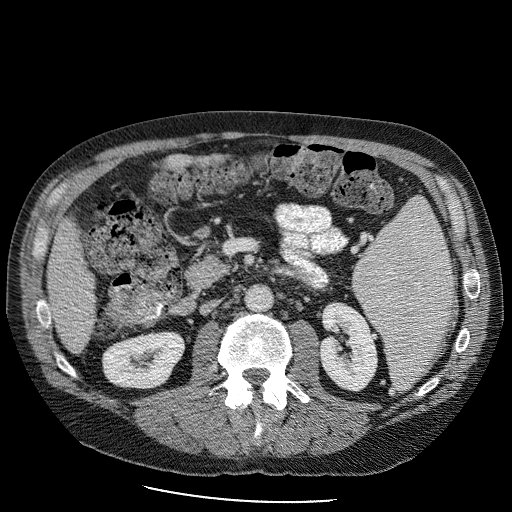
Contrast-enhanced abdominal CT (liver protocol), one axial slice; slice 30 of 98 in the series (ordered by position); reconstruction kernel STANDARD; 120 kVp; soft-tissue window (W 400 / L 40 HU); 2.5 mm slice thickness; 512 × 512 image matrix, field of view 400 × 400 mm. From the clinical record (not read from this slice): diagnosis: hepatocellular carcinoma (patient treated with transarterial chemoembolisation; whether this scan precedes or follows treatment is not stated here); TNM stage (as recorded): Stage-II; Child-Pugh class: B; tumour differentiation: moderately differentiated.
Structures marked on this image (semi-automatic segmentation, software-assisted and operator-edited):
- liver parenchyma outside the tumour (the mass and vessels are separate outlines, so this box may not span the whole liver): bounding box <46,148,236,350> (left, top, right, bottom; pixels)